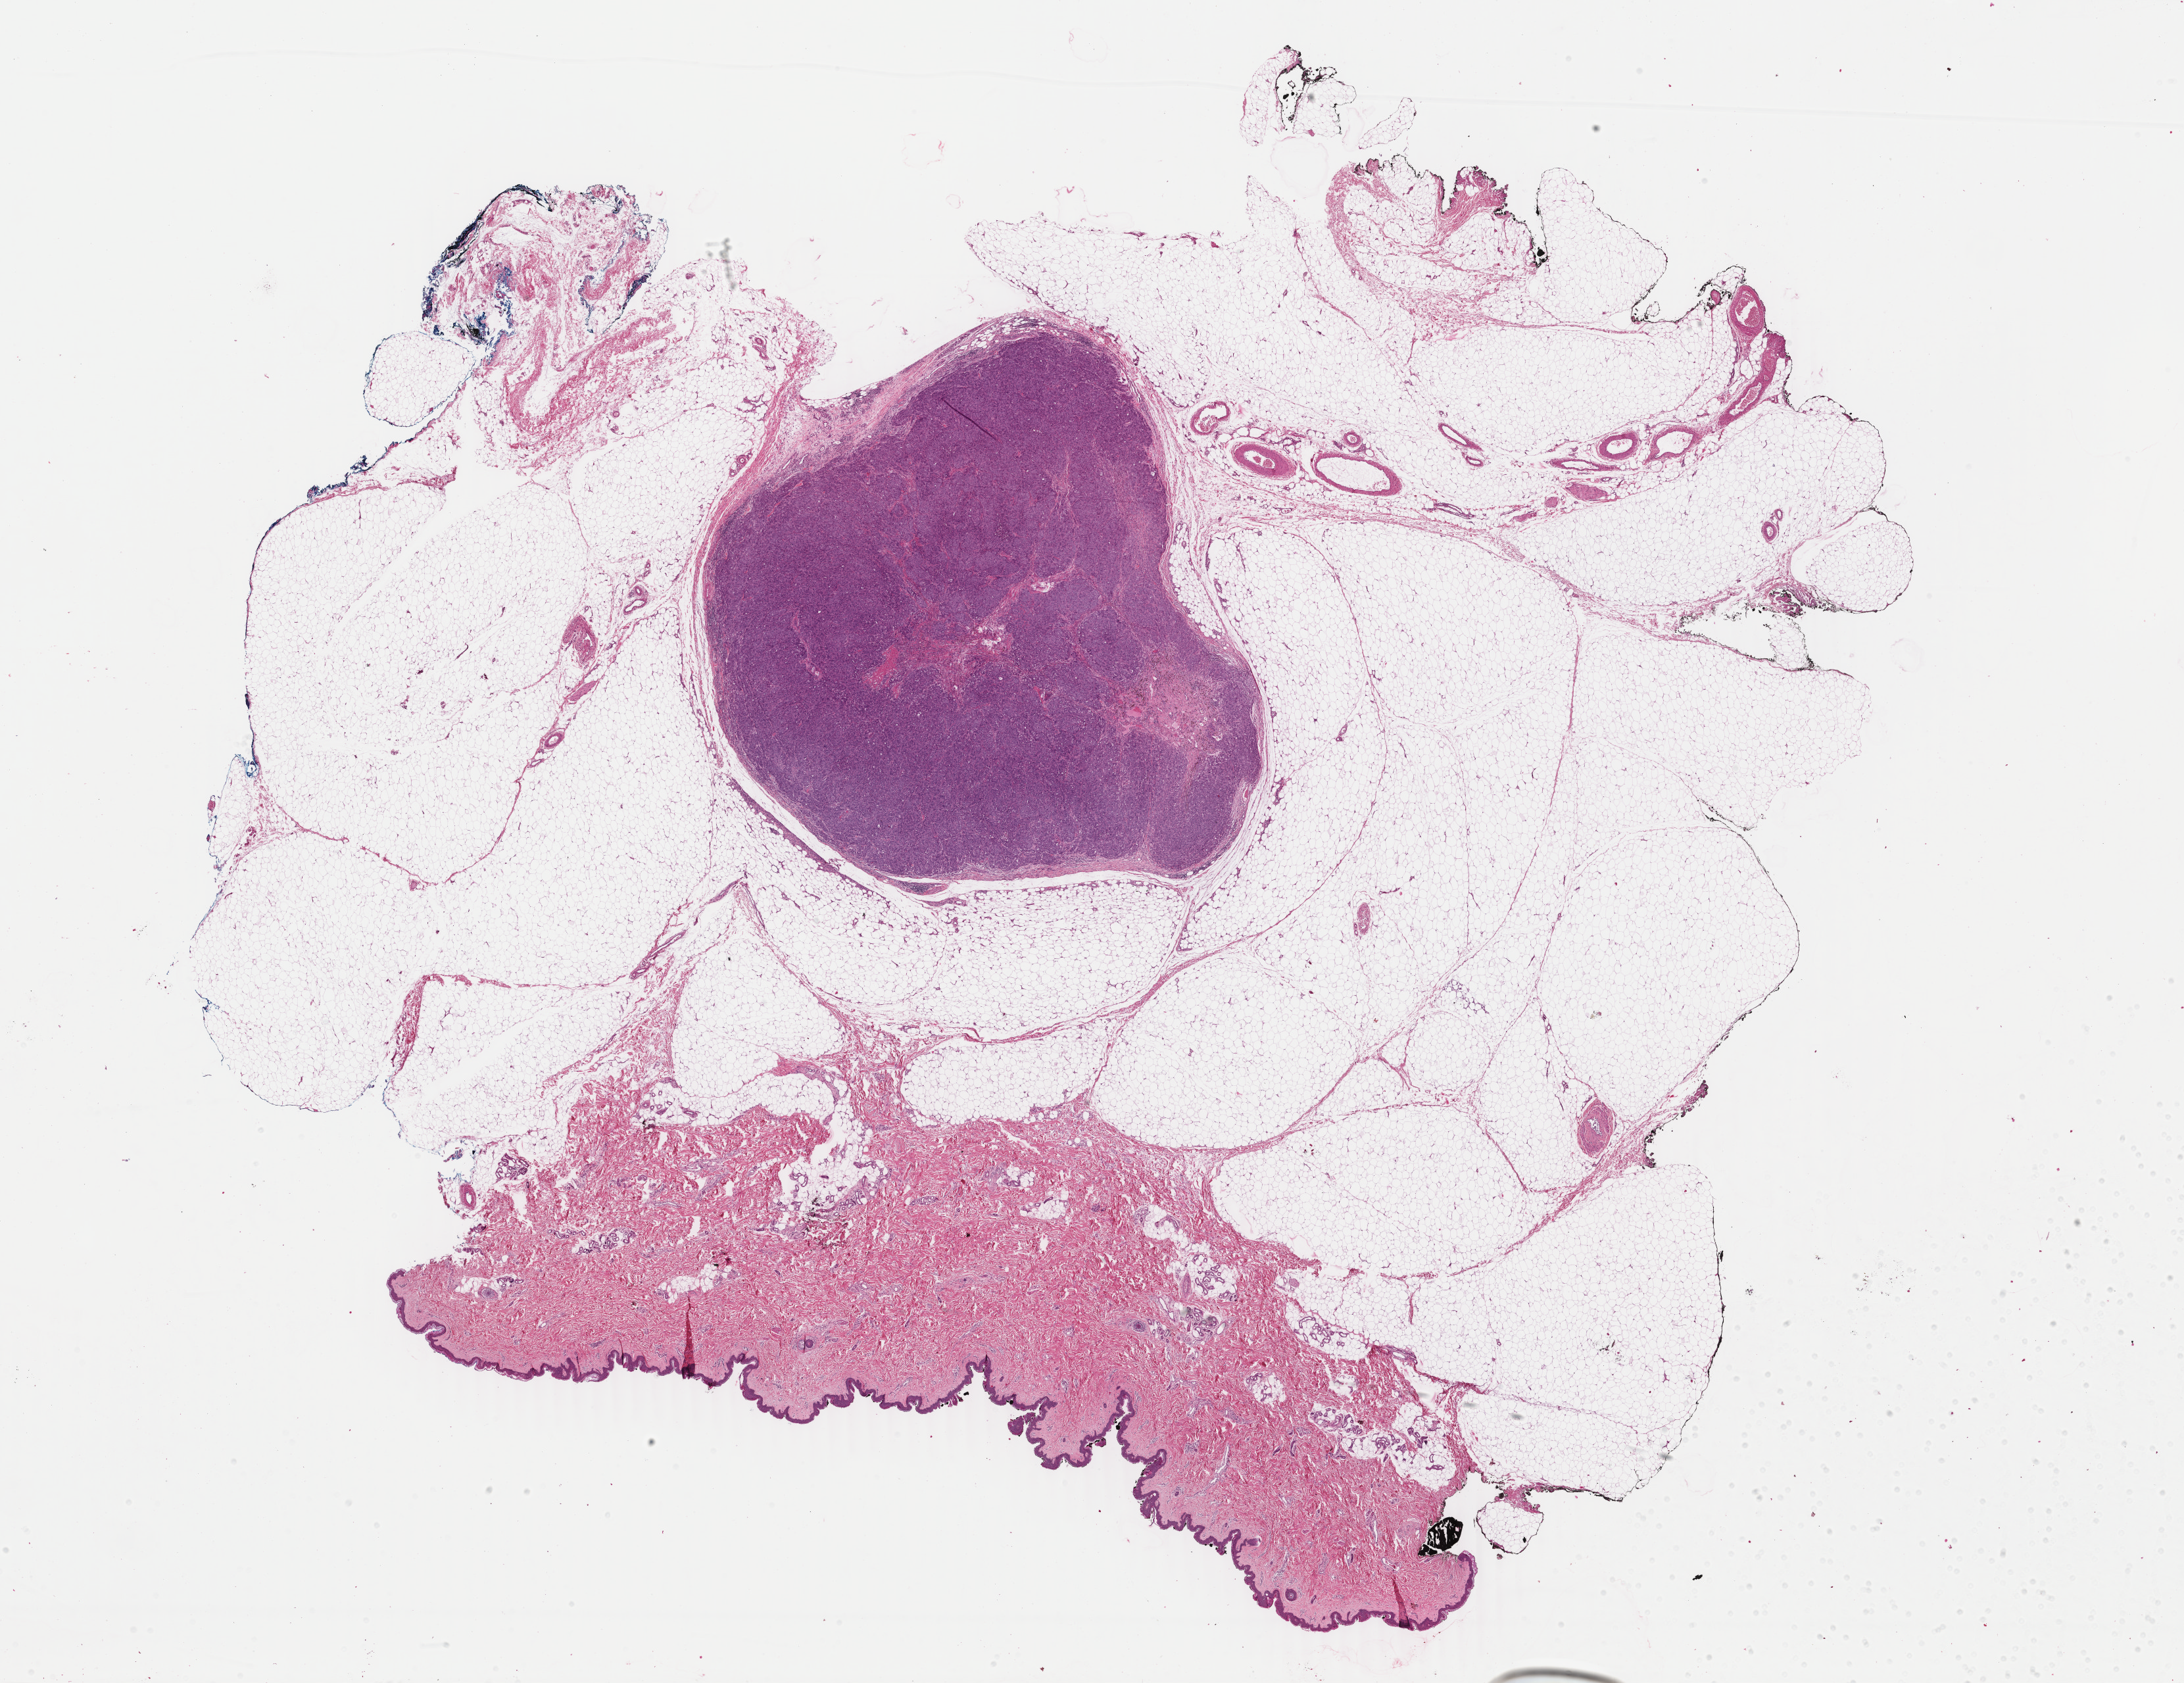
Whole-slide histology image, H&E-stained, shown as a low-resolution overview of the whole scanned area (about 26.4 x 20.4 mm); formalin-fixed paraffin-embedded (FFPE) diagnostic section; sample: primary tumour, skin. Patient: male, age at initial diagnosis 43 years.
Diagnosis: Malignant melanoma, NOS.